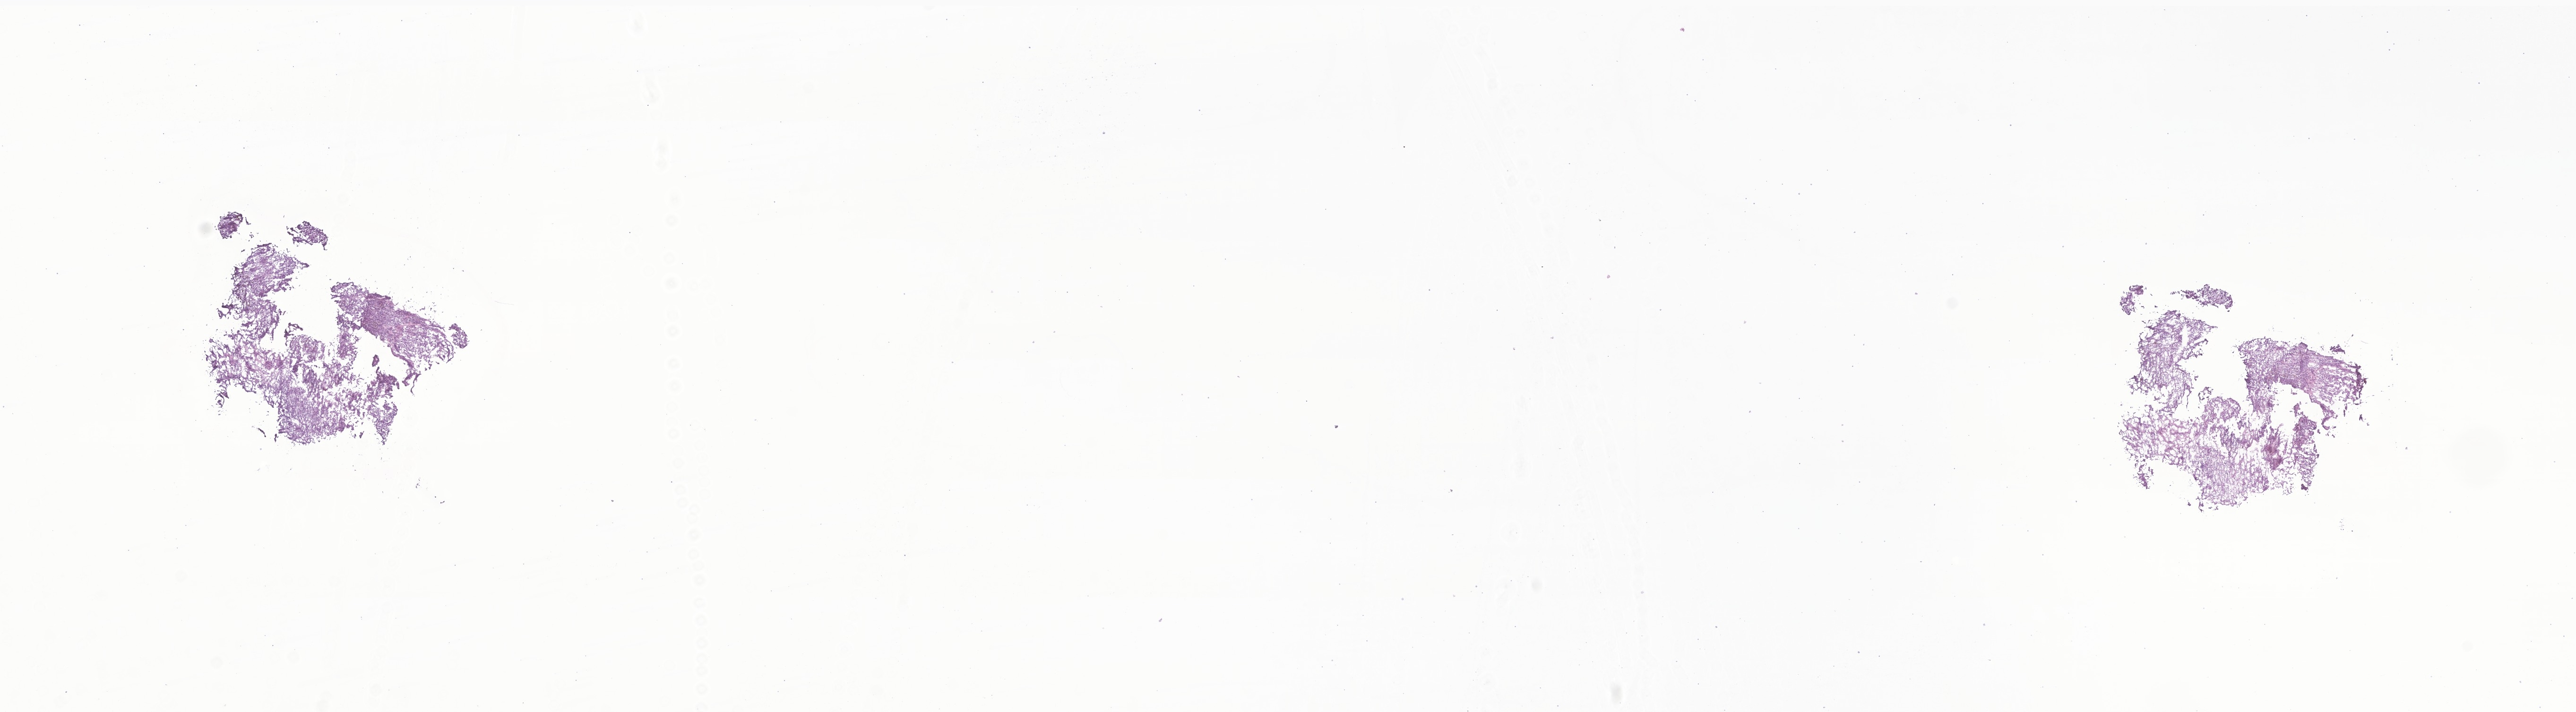
Hematoxylin and eosin (H&E) whole-slide image of tumor tissue from the soft tissue of lower extremity — low-resolution overview of the scanned area, about 23.0 x 6.4 mm. Frozen section (OCT-embedded). Female patient, age 98 months (8 years 2 months).
Diagnosis (ICD-O-3 morphology term): Angiomatoid fibrous histiocytoma.